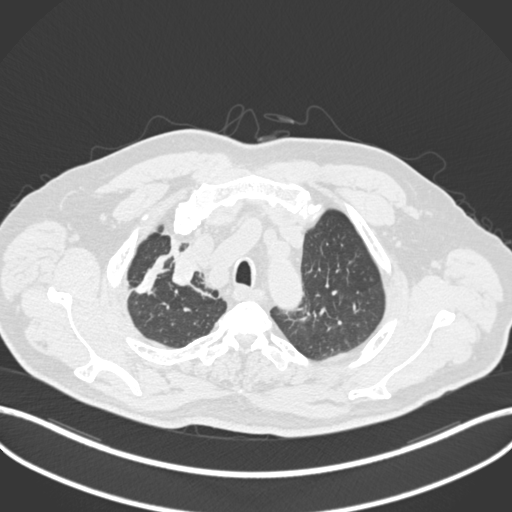
Chest CT, one axial slice; position 169 of 255 along the scan axis; reconstruction kernel B30f; lung window (W 1500 / L -600 HU); 1 mm slice thickness; 512 × 512 image matrix, field of view 400 × 400 mm. Male patient, age 60 years. Case-level facts recorded for this patient, not image findings: clinical TNM (as recorded): T1b N1 M0.
Outlined on this slice (bounding box drawn by a radiologist):
- lung tumour (recorded histology: squamous cell carcinoma): bounding box <166,239,201,297> (left, top, right, bottom; pixels)